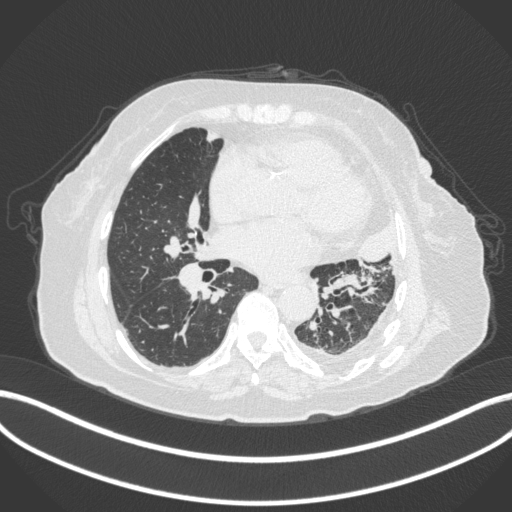
Chest CT, one axial slice; position 171 of 399 along the scan axis; 120 kVp; lung window (W 1500 / L -600 HU); 1 mm slice thickness; 512 × 512 image matrix. Female patient, age 75 years. From the clinical record (not read from this slice): clinical TNM (as recorded): T3 N3 M1.
Outlined on this slice (bounding box drawn by a radiologist):
- lung tumour (recorded histology: adenocarcinoma): bounding box [x1, y1, x2, y2] px = [360, 222, 401, 269]